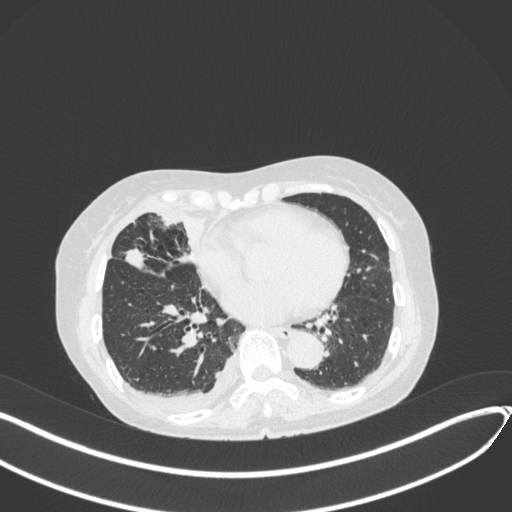
Chest CT, one axial slice. Position 157 of 418 along the scan axis. 120 kVp. Lung window (W 1500 / L -600 HU). 1 mm slice thickness. 512 × 512 image matrix, field of view 400 × 400 mm. Patient: female, 75 years. Case-level facts recorded for this patient, not image findings: clinical TNM (as recorded): T2a N3 M0.
Outlined on this slice (bounding box drawn by a radiologist):
- lung tumour (recorded histology: adenocarcinoma): bounding box (x1, y1, x2, y2) in pixels: (123, 248, 149, 271)